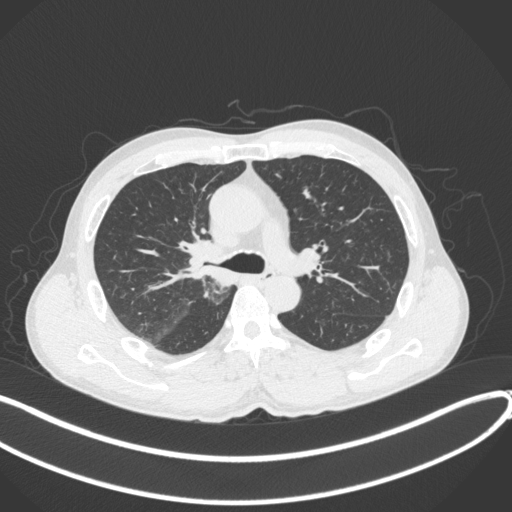
Chest CT, one axial slice. Position 253 of 409 along the scan axis. Reconstruction kernel B31f. 120 kVp. Lung window (W 1500 / L -600 HU). 1 mm slice thickness. 512 × 512 image matrix, field of view 400 × 400 mm. Male patient, age 53 years. From the clinical record (not read from this slice): clinical TNM (as recorded): T1b N0 M0.
Annotated regions visible in this slice (rectangle marked by the reading radiologist):
- lung tumour (recorded histology: squamous cell carcinoma): bounding box <180,238,230,285> (left, top, right, bottom; pixels)